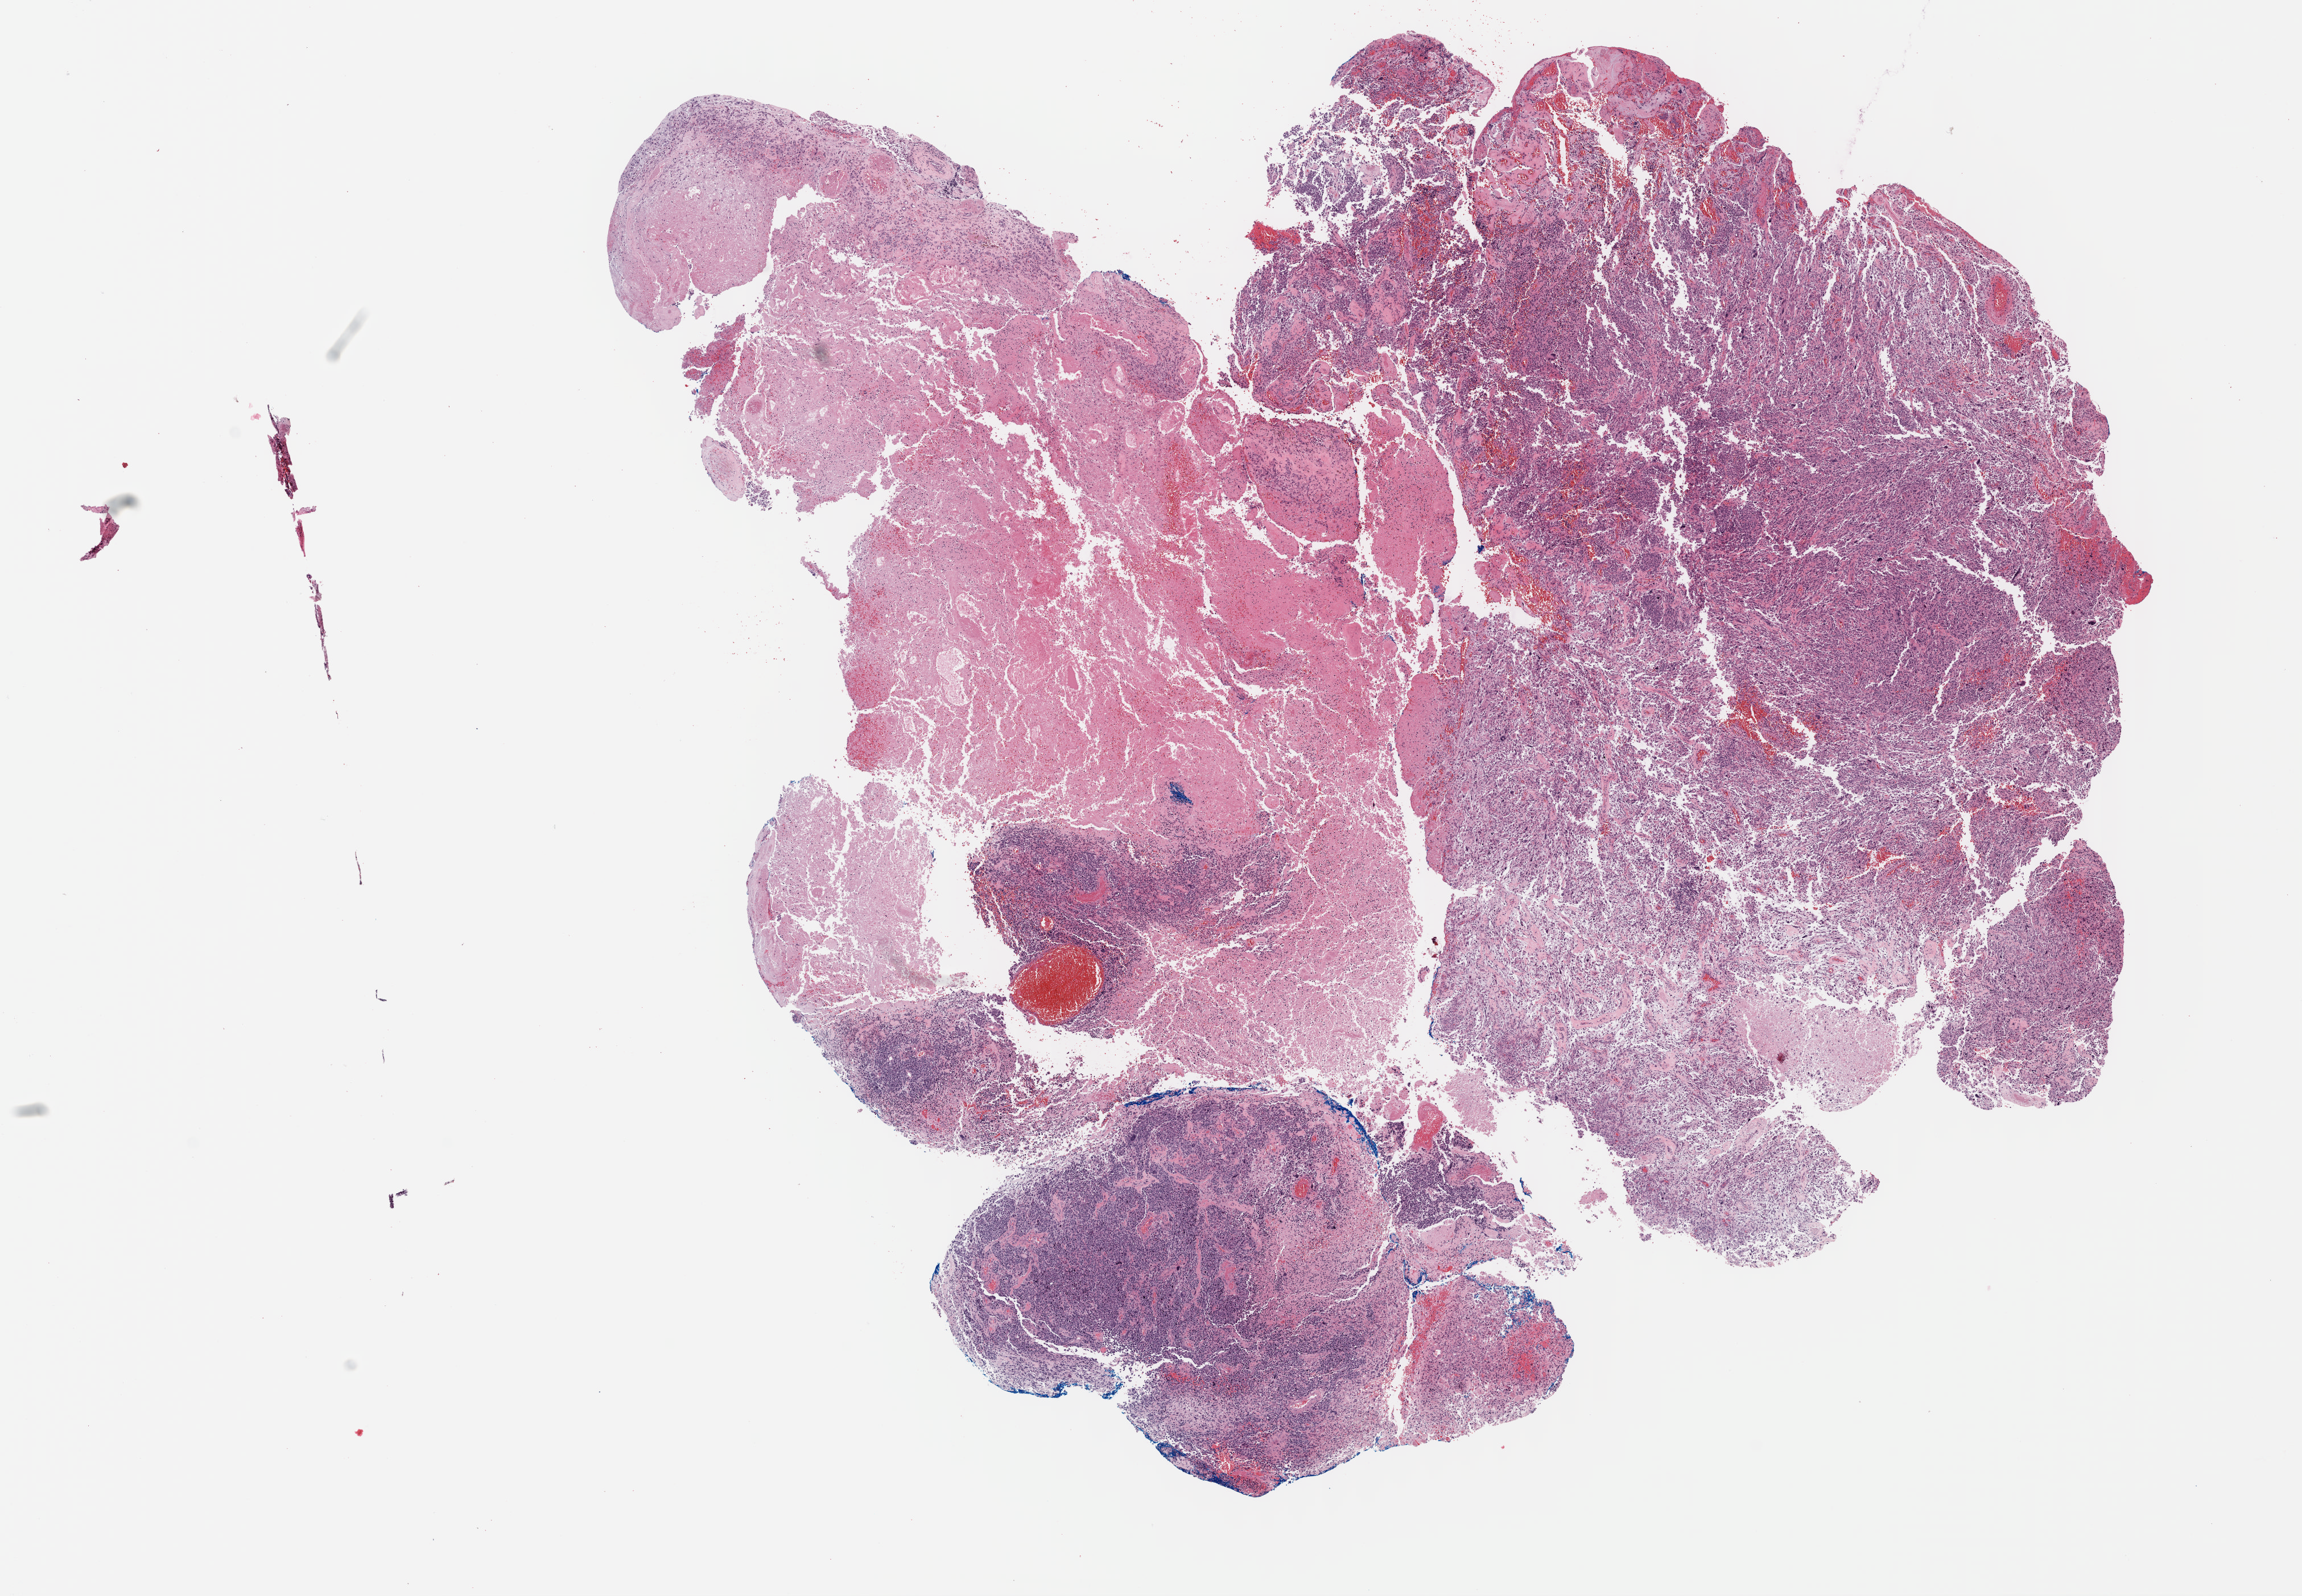
H&E whole-slide image — shown as a low-resolution overview of the whole scanned area (about 15.9 x 11.0 mm). Formalin-fixed paraffin-embedded (FFPE) diagnostic section. Sample: primary tumour, brain. Male patient; age at initial diagnosis 39 years.
• pathologic diagnosis: Glioblastoma